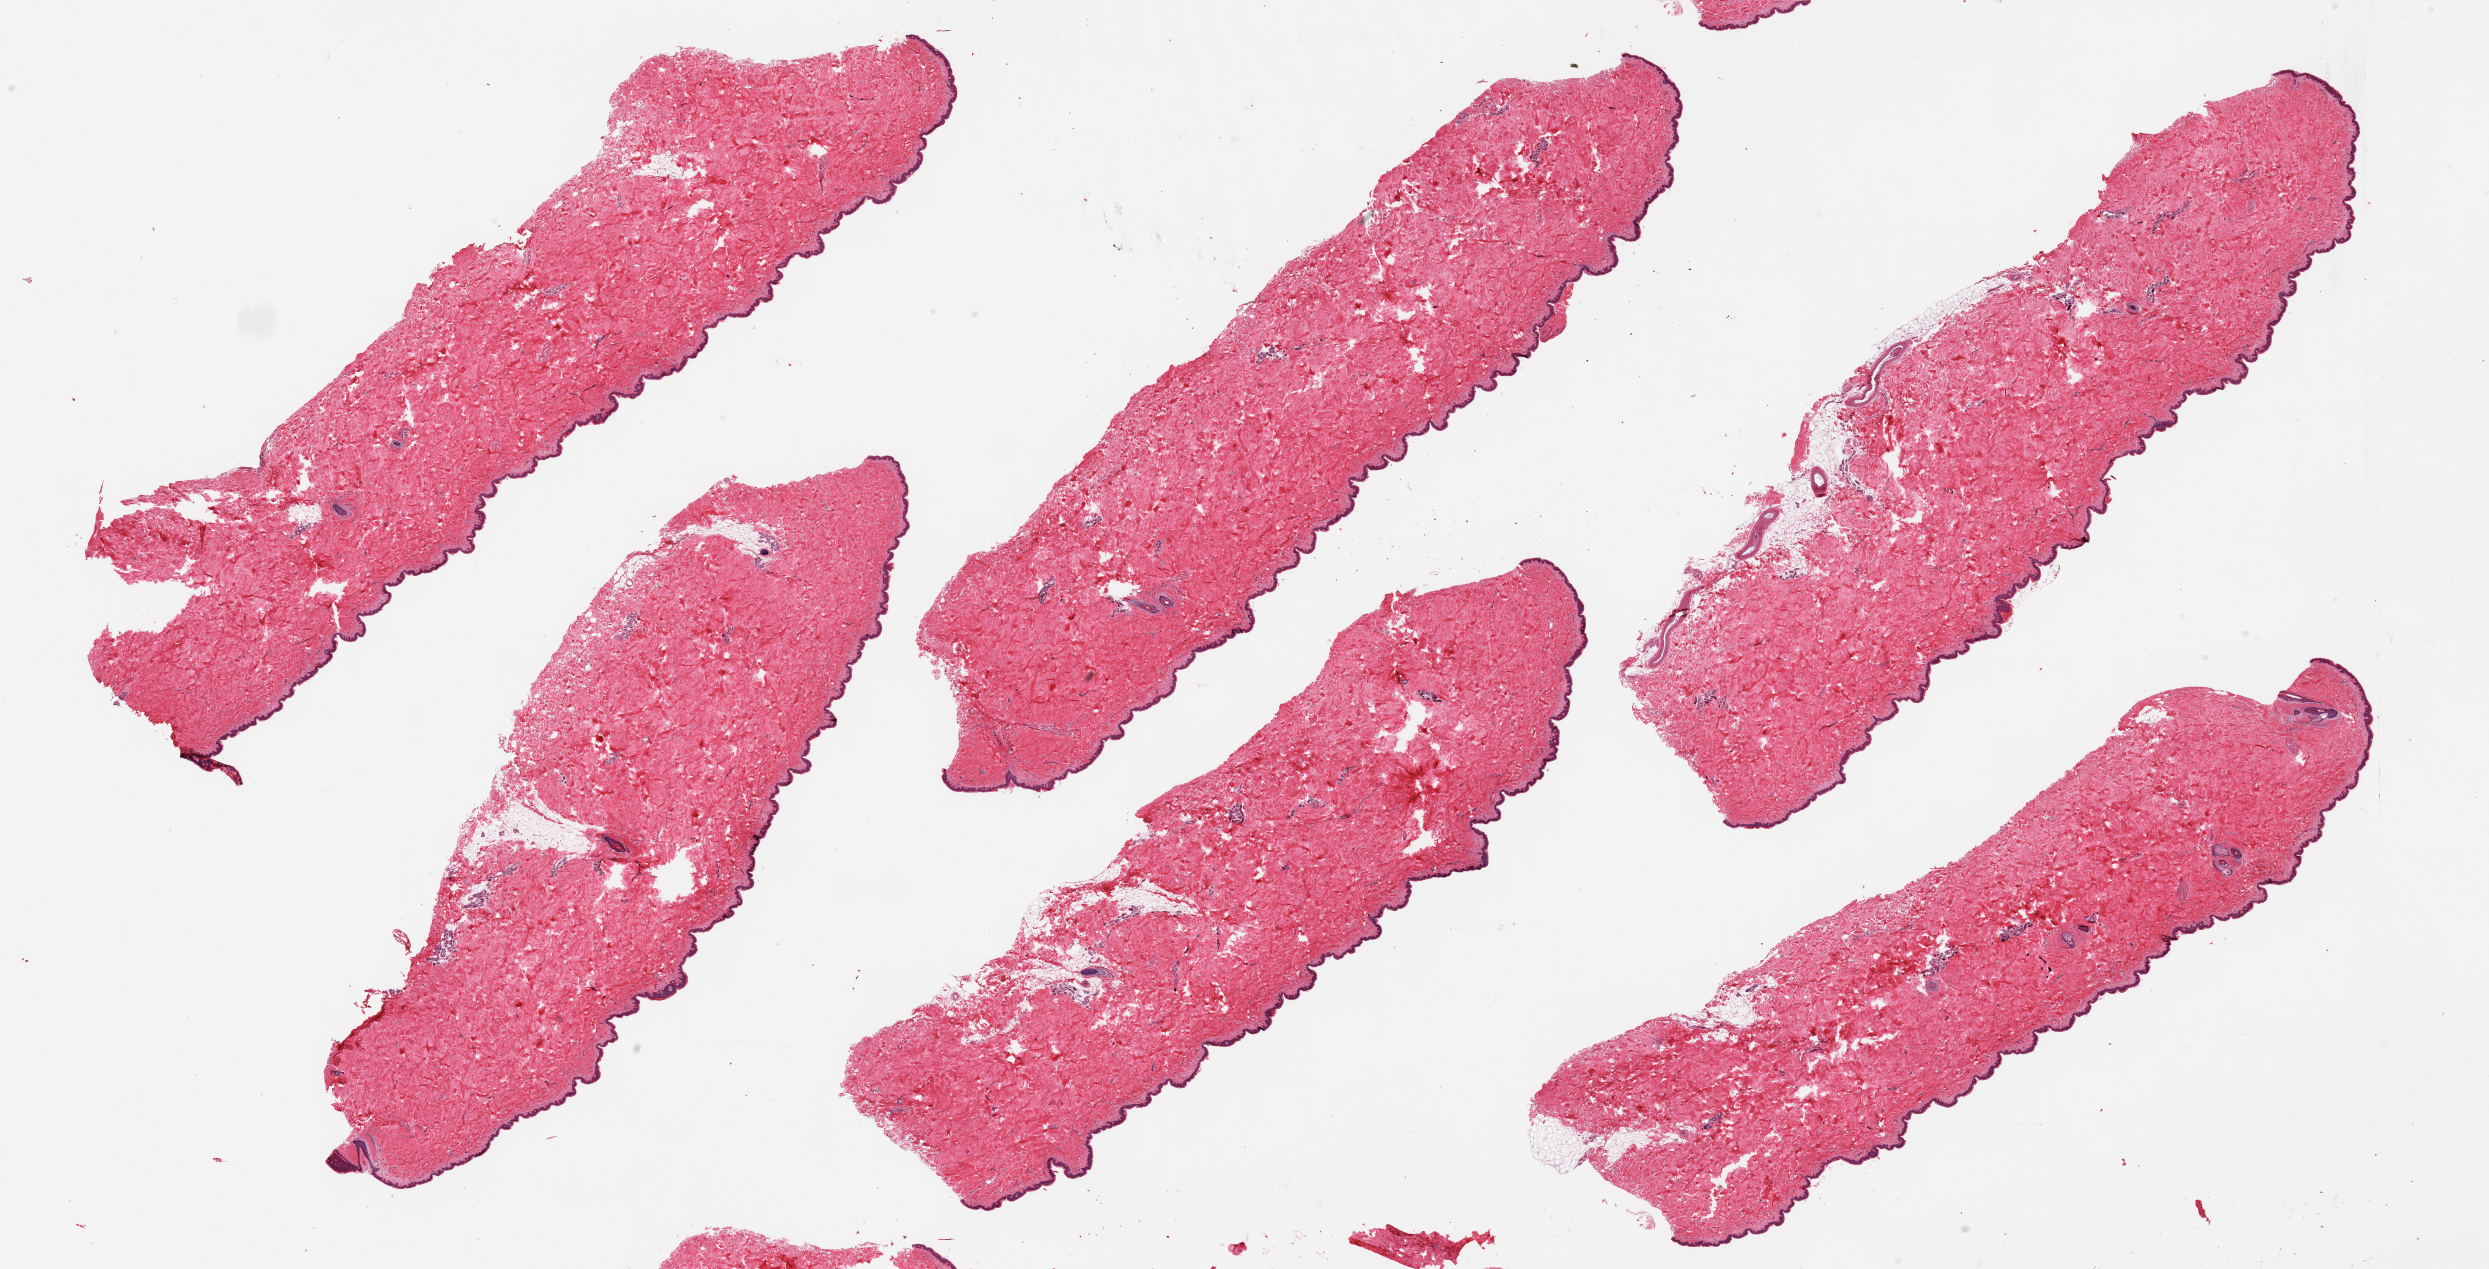
Digitized hematoxylin and eosin (H&E)-stained section, brightfield — shown as a low-resolution overview of the whole scanned area (about 39.4 x 20.1 mm), PAXgene-fixed, paraffin-embedded tissue, sampled site (target tissue): skin of suprapubic region, tissue donor sample. Female donor.
- review note (as recorded): 6 pieces, well dissected